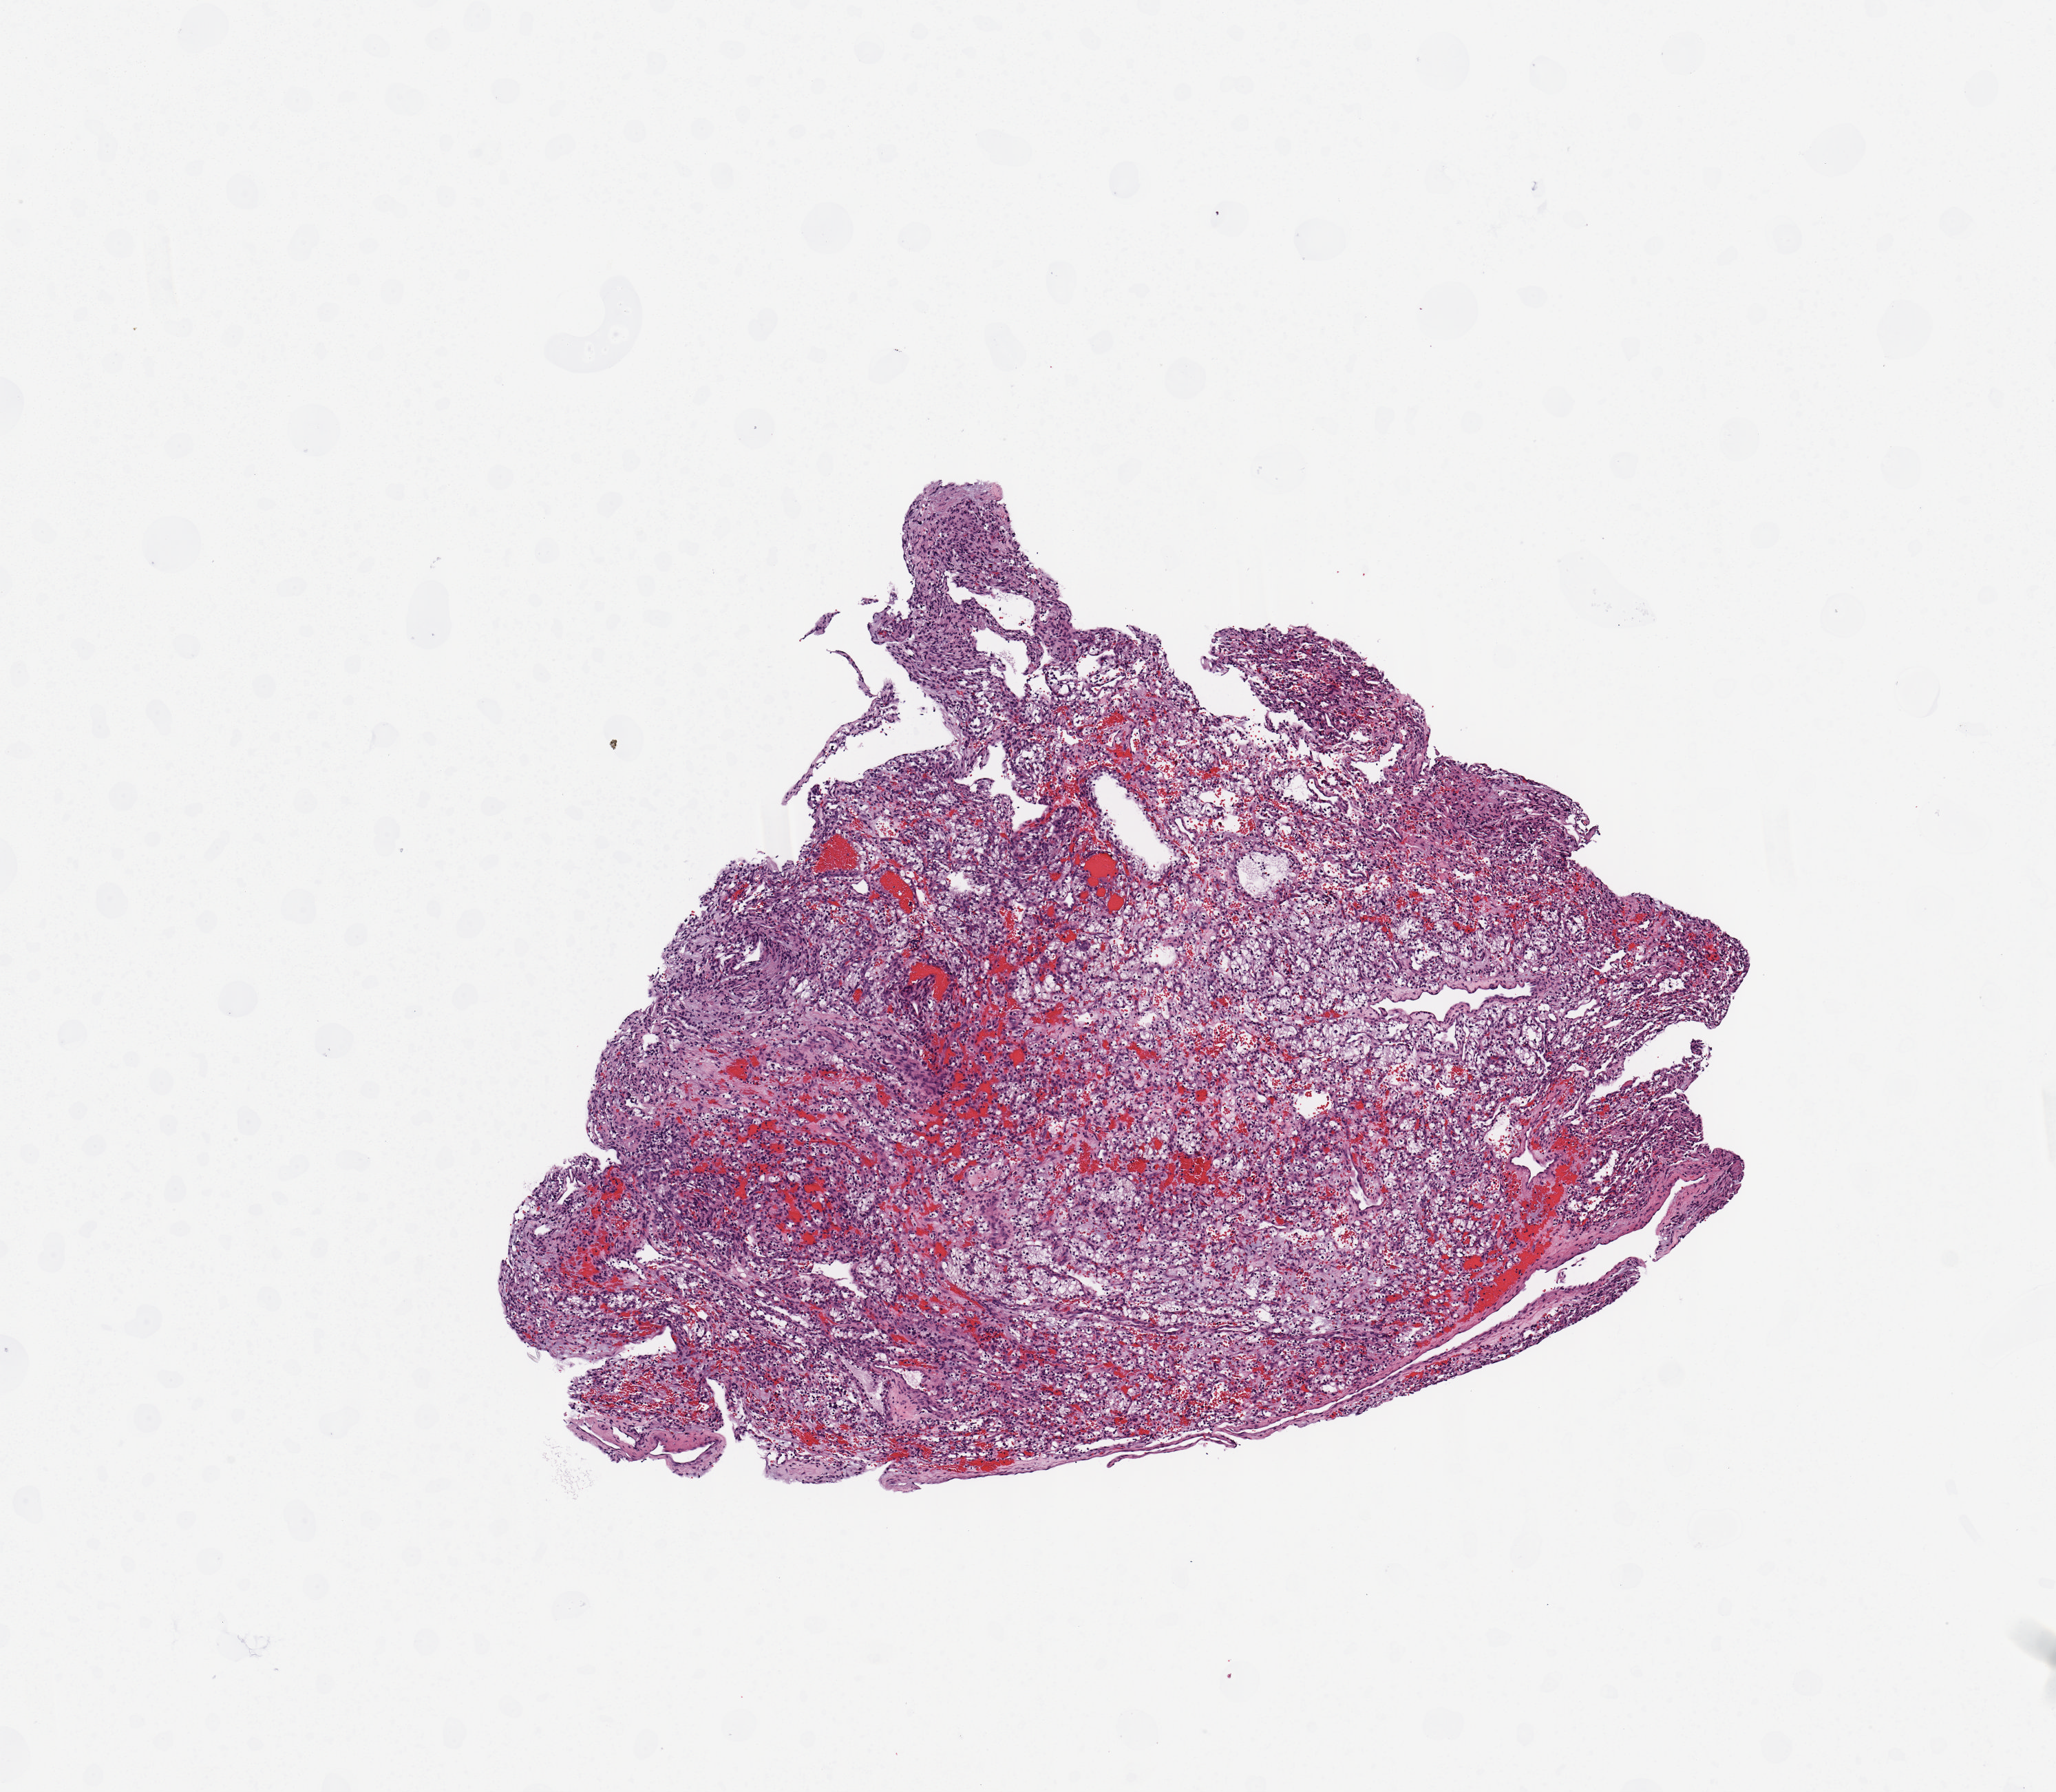
Hematoxylin and eosin (H&E) stained whole-slide image, shown as a low-resolution overview of the whole scanned area (about 5.9 x 5.1 mm, from a 20x scan). Tumour tissue sample, kidney. Female, 33 y/o.
Histologic diagnosis: Renal cell carcinoma, NOS.